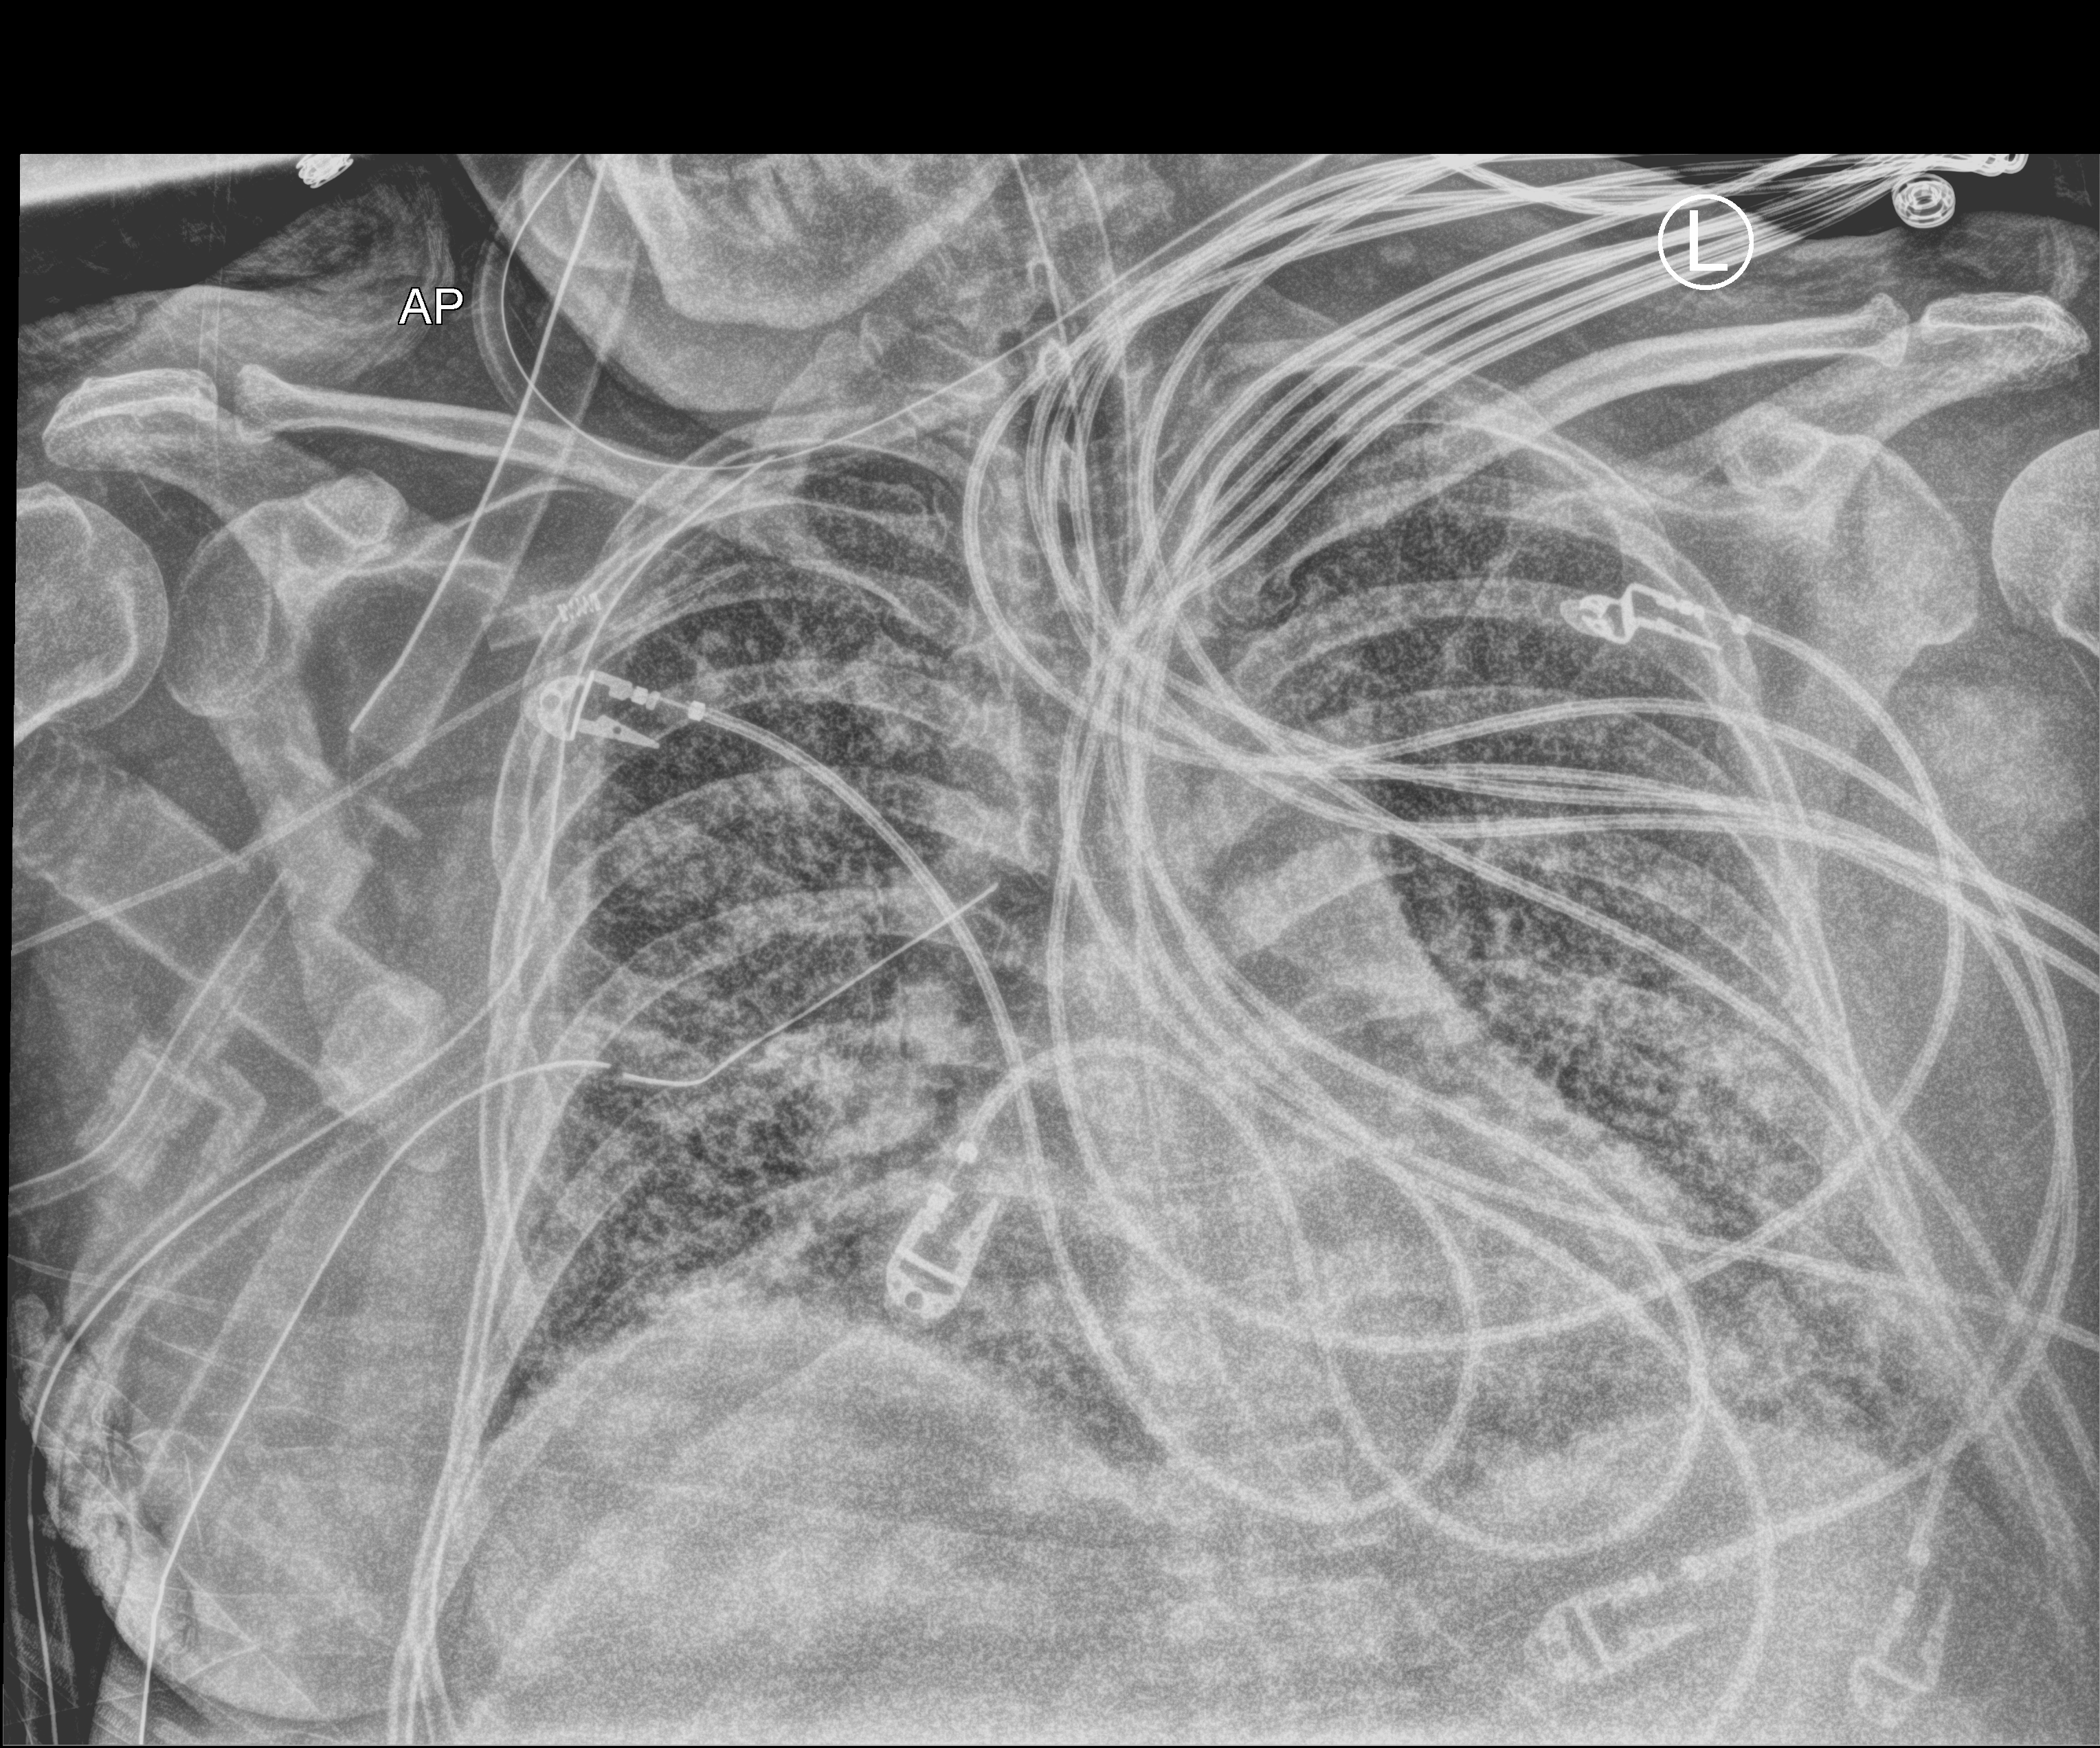
Portable chest radiograph, anteroposterior (AP) projection. Patient hospitalised with COVID-19, aged 18–59 years.
From the hospital-stay record, not from the radiograph (when in the stay this image was taken is not recorded): mechanically ventilated during this hospital stay: yes.